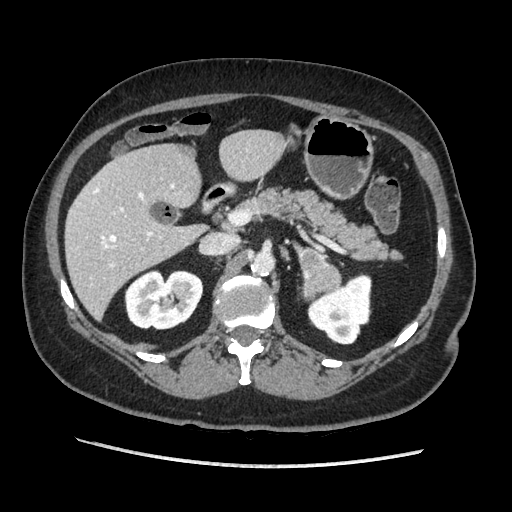
Contrast-enhanced abdominal CT, one axial slice. Soft-tissue window (W 400 / L 40 HU). 1.25 mm slice thickness. 512 × 512 image matrix, field of view 360 × 360 mm. Female patient. From the clinical record (not read from this slice): diagnosis: adrenocortical carcinoma; tumour side: left adrenal; tumour size at pathology: 6.5 cm; Ki-67 index: 22 %; stage (as recorded): 2.
Structures marked on this image (semi-automatic segmentation, software-assisted and operator-edited):
- mass: bounding box (x1, y1, x2, y2) in pixels: (301, 249, 342, 297)